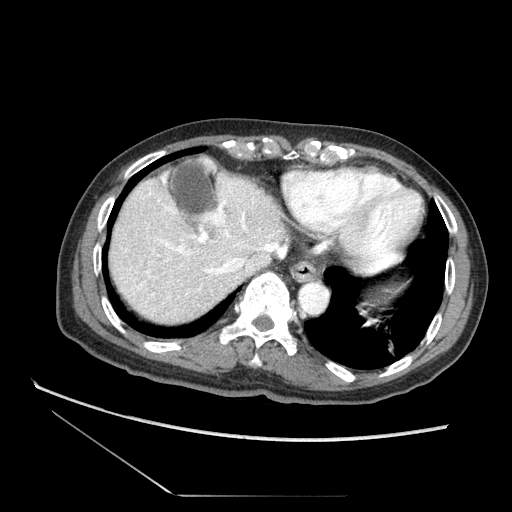
Contrast-enhanced abdominal CT (liver protocol), one axial slice; position 64 of 73 along the scan axis; soft-tissue window (W 400 / L 40 HU); 2.5 mm slice thickness; 512 × 512 image matrix. From the clinical record (not read from this slice): diagnosis: hepatocellular carcinoma (patient treated with transarterial chemoembolisation; whether this scan precedes or follows treatment is not stated here); TNM stage (as recorded): Stage-II; Child-Pugh class: A; tumour size: 3.8 cm.
Structures marked on this image (semi-automatically segmented with operator editing):
- abdominal aorta: bounding box <300,283,329,313> (left, top, right, bottom; pixels)
- liver parenchyma outside the tumour (the mass and vessels are separate outlines, so this box may not span the whole liver): <108,172,427,332>
- mass: <114,270,158,300>
- liver vessels: <157,216,215,277>